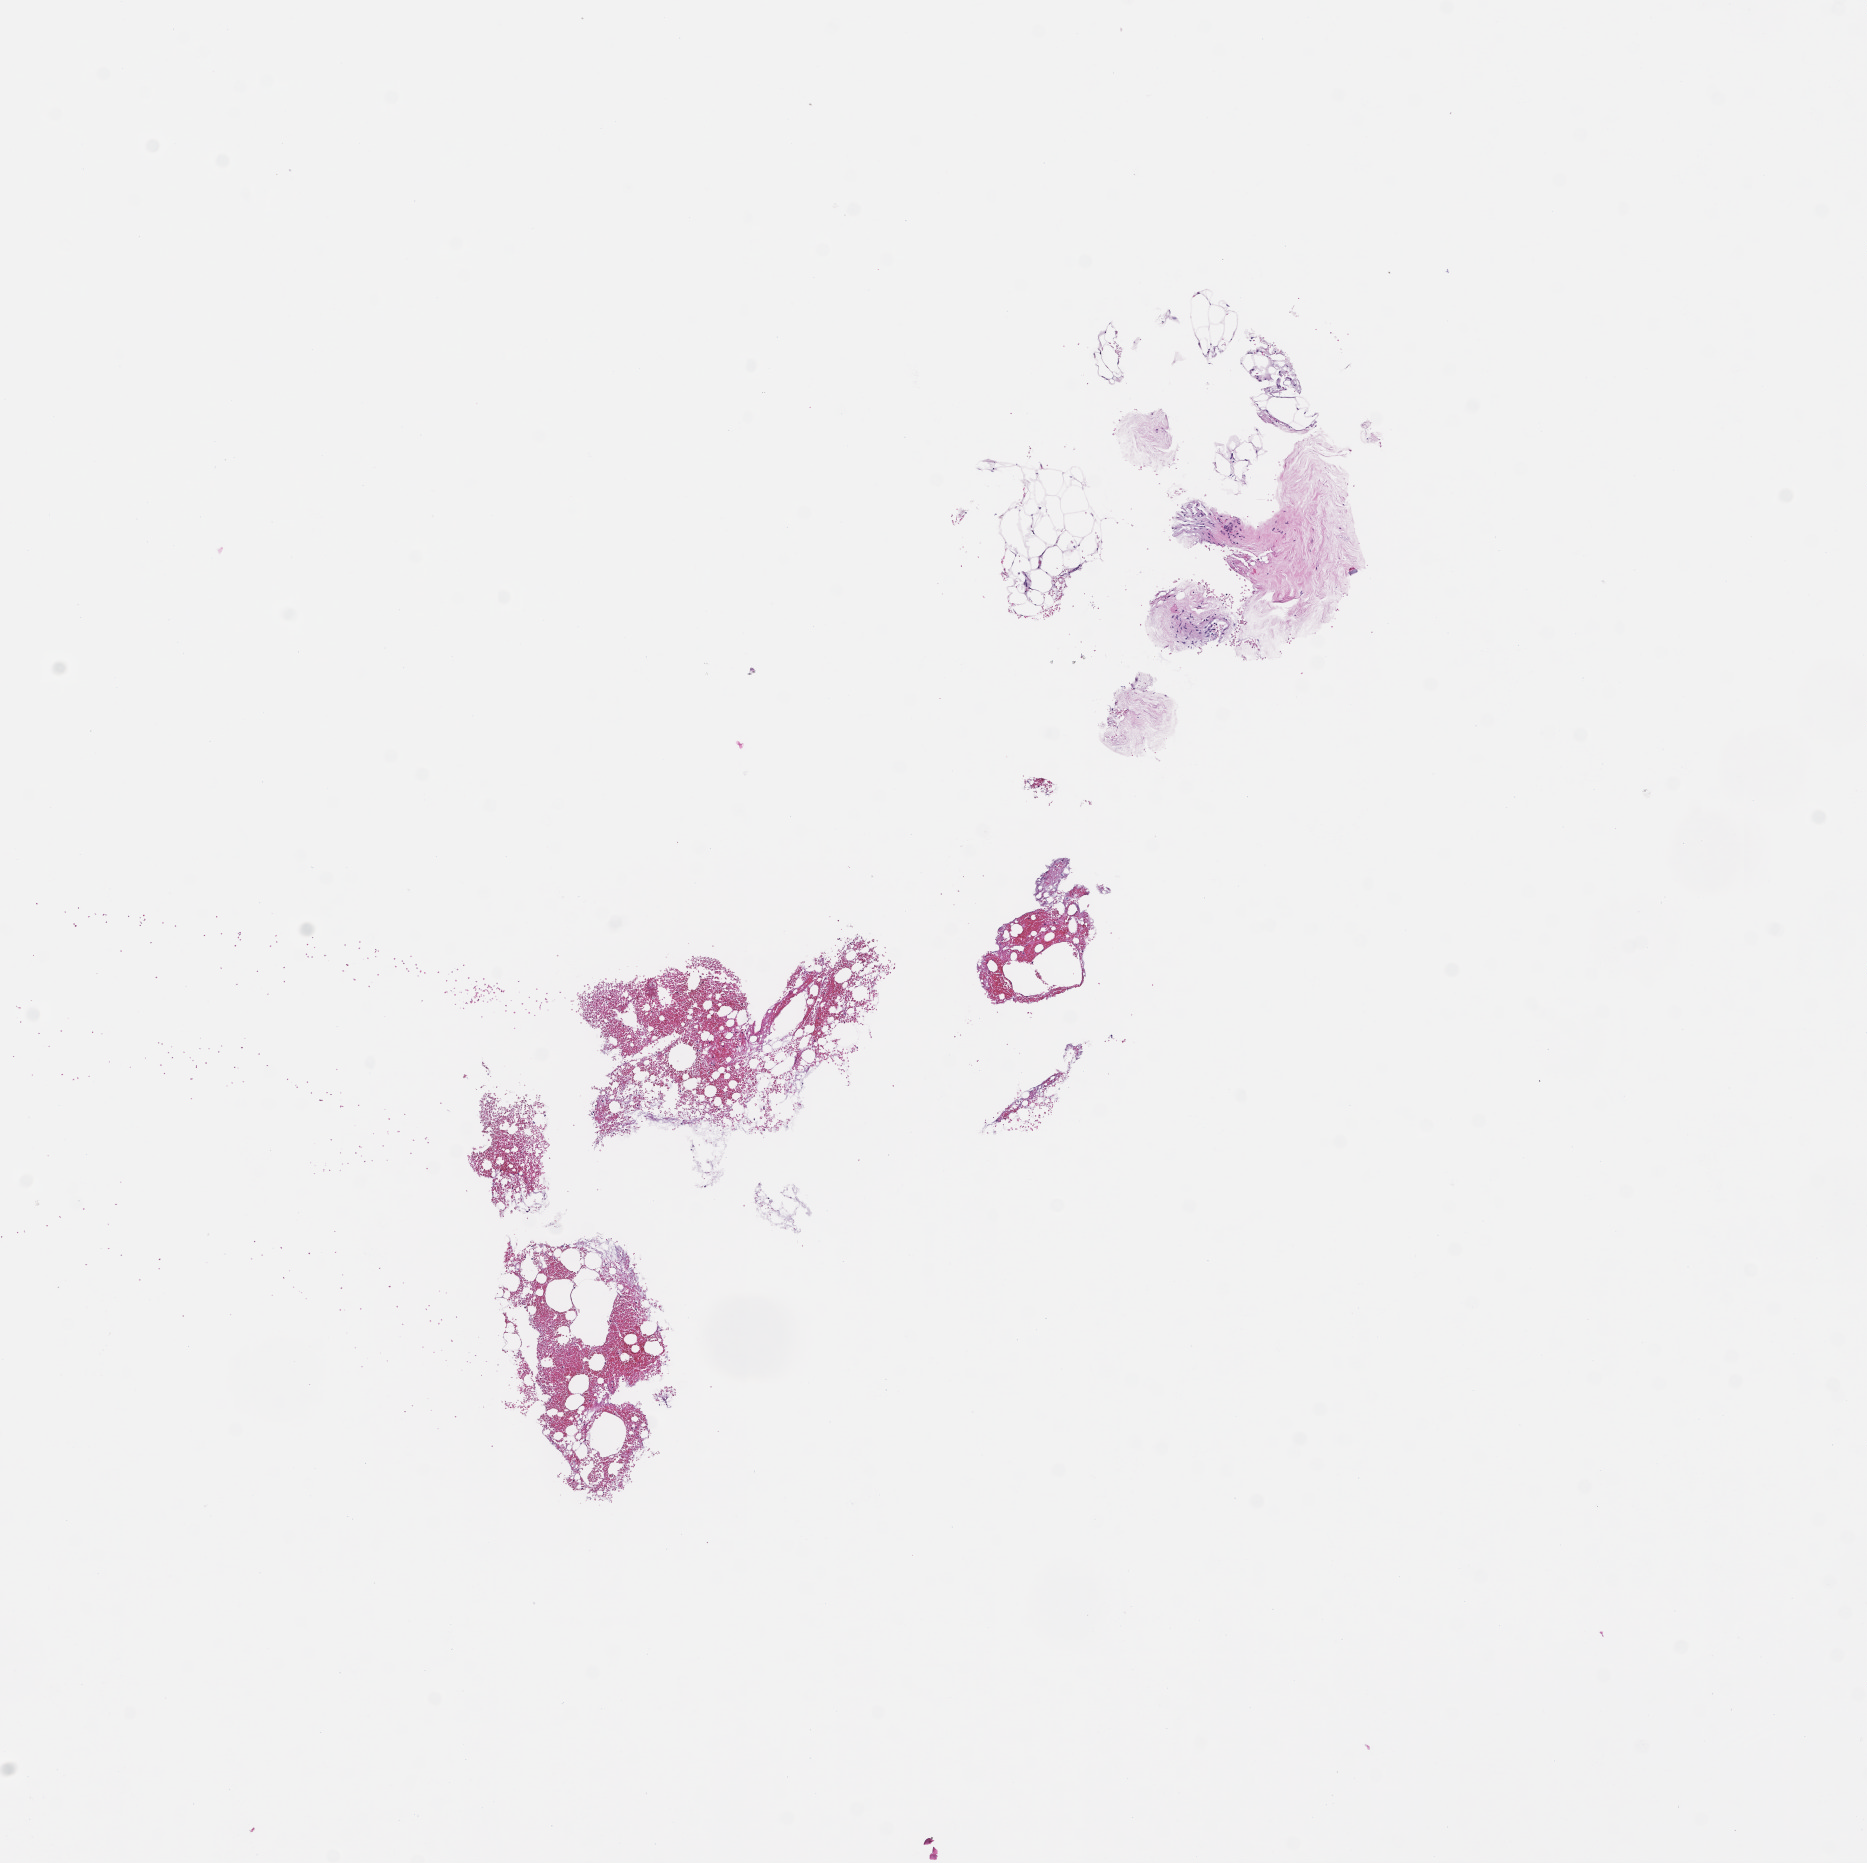
Hematoxylin and eosin (H&E) whole-slide image, whole scanned area (about 7.5 x 7.5 mm) shown as a low-resolution overview. FFPE section. Site: breast. Specimen time point: collected at baseline (before treatment). Patient sex: female.
This section: primary tumour tissue. Diagnosis: Invasive Breast Carcinoma.